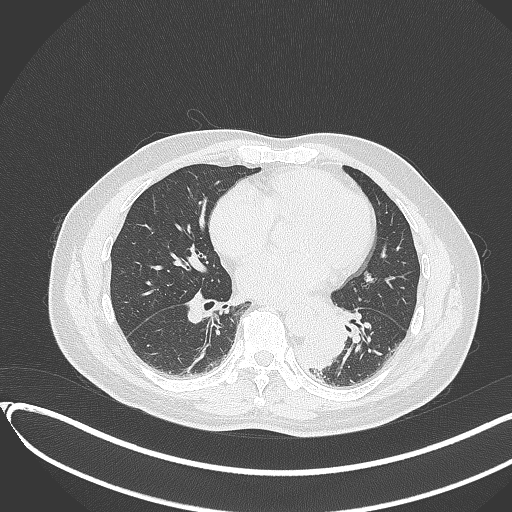
Chest CT, one axial slice; slice 144 of 417 in the series (ordered by position); reconstruction kernel B70f; lung window (W 1500 / L -600 HU); 1 mm slice thickness; 512 × 512 image matrix. Male patient, age 54 years. From the clinical record (not read from this slice): clinical TNM (as recorded): T3 N0 M0.
Annotated regions visible in this slice (rectangle marked by the reading radiologist):
- lung tumour (recorded histology: squamous cell carcinoma): box from (x=300, y=325) to (x=348, y=361) px